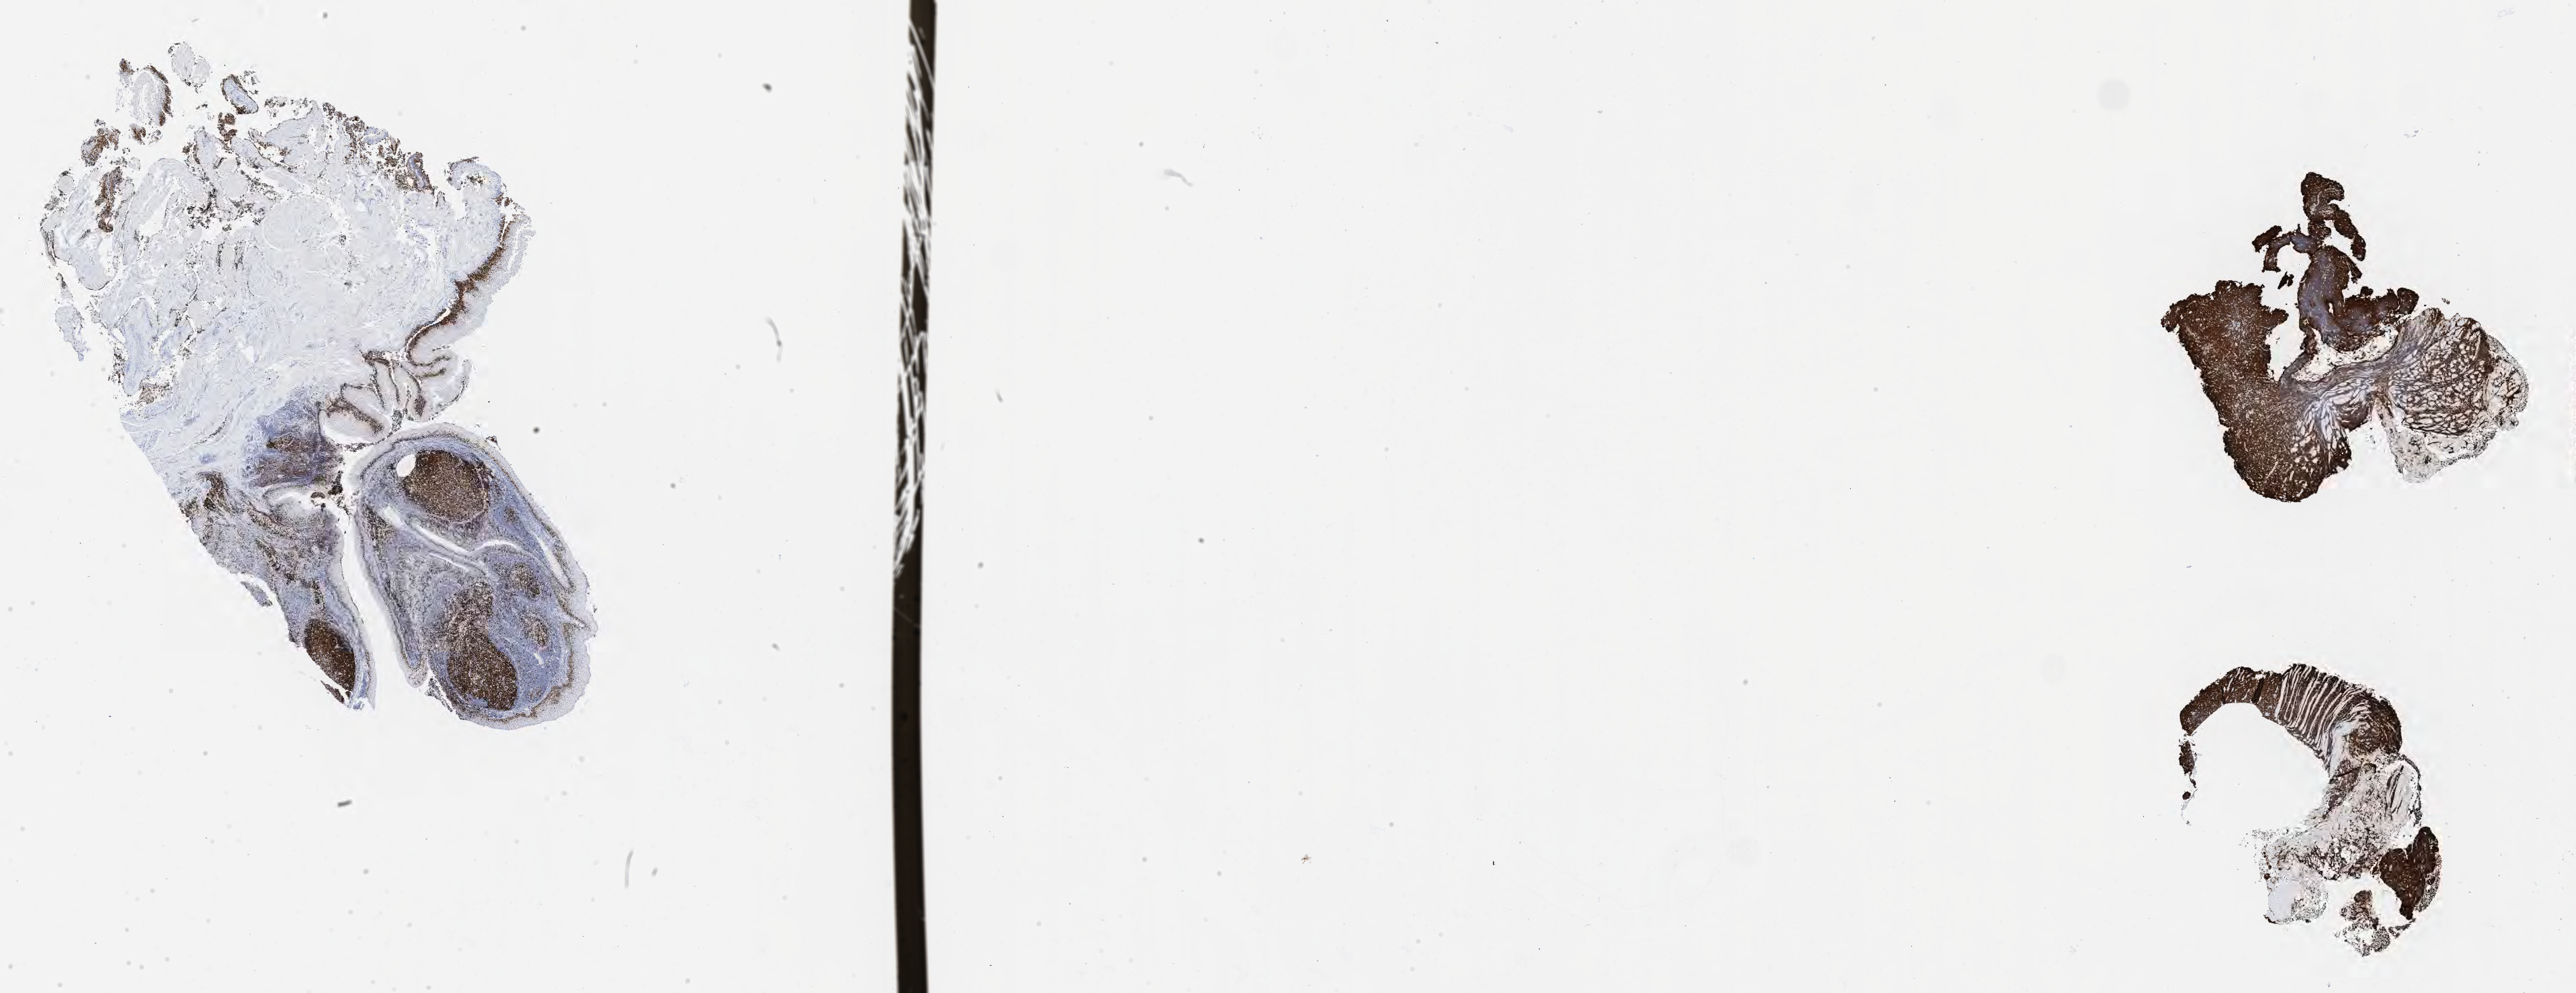
Whole-slide image, immunohistochemical stain for Ki-67, a low-resolution overview of the entire scanned area, about 30.7 x 11.8 mm. Specimen: tumor tissue. Site: lymph node of head and neck. Male patient, 73 years old.
- histologic diagnosis: Burkitt lymphoma, NOS